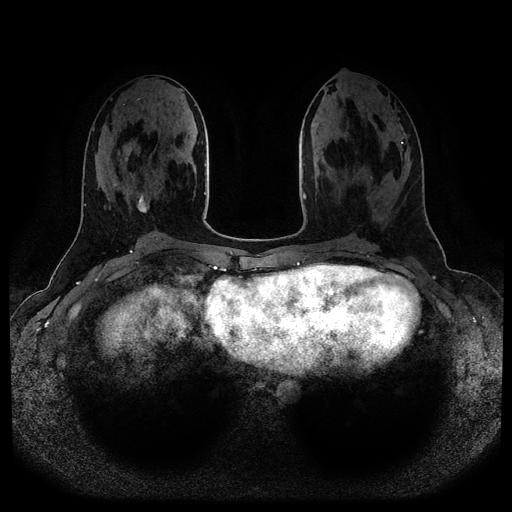
Breast MRI (dynamic contrast-enhanced, multi-phase), one axial slice. Position 43 of 116 along the scan axis. Dynamic contrast-enhanced series, time point 2 of 5 at this slice position (early post-contrast). 1.5 T. TE 2.6 ms, TR 5.2 ms. 2 mm slice thickness. 512 × 512 image matrix, field of view 380 × 380 mm. Patient: female, 25 years.
Outlined on this slice (semi-automatic segmentation, software-assisted and operator-edited):
- breast lesion (labelled benign in the annotation): box from (x=137, y=193) to (x=151, y=213) px